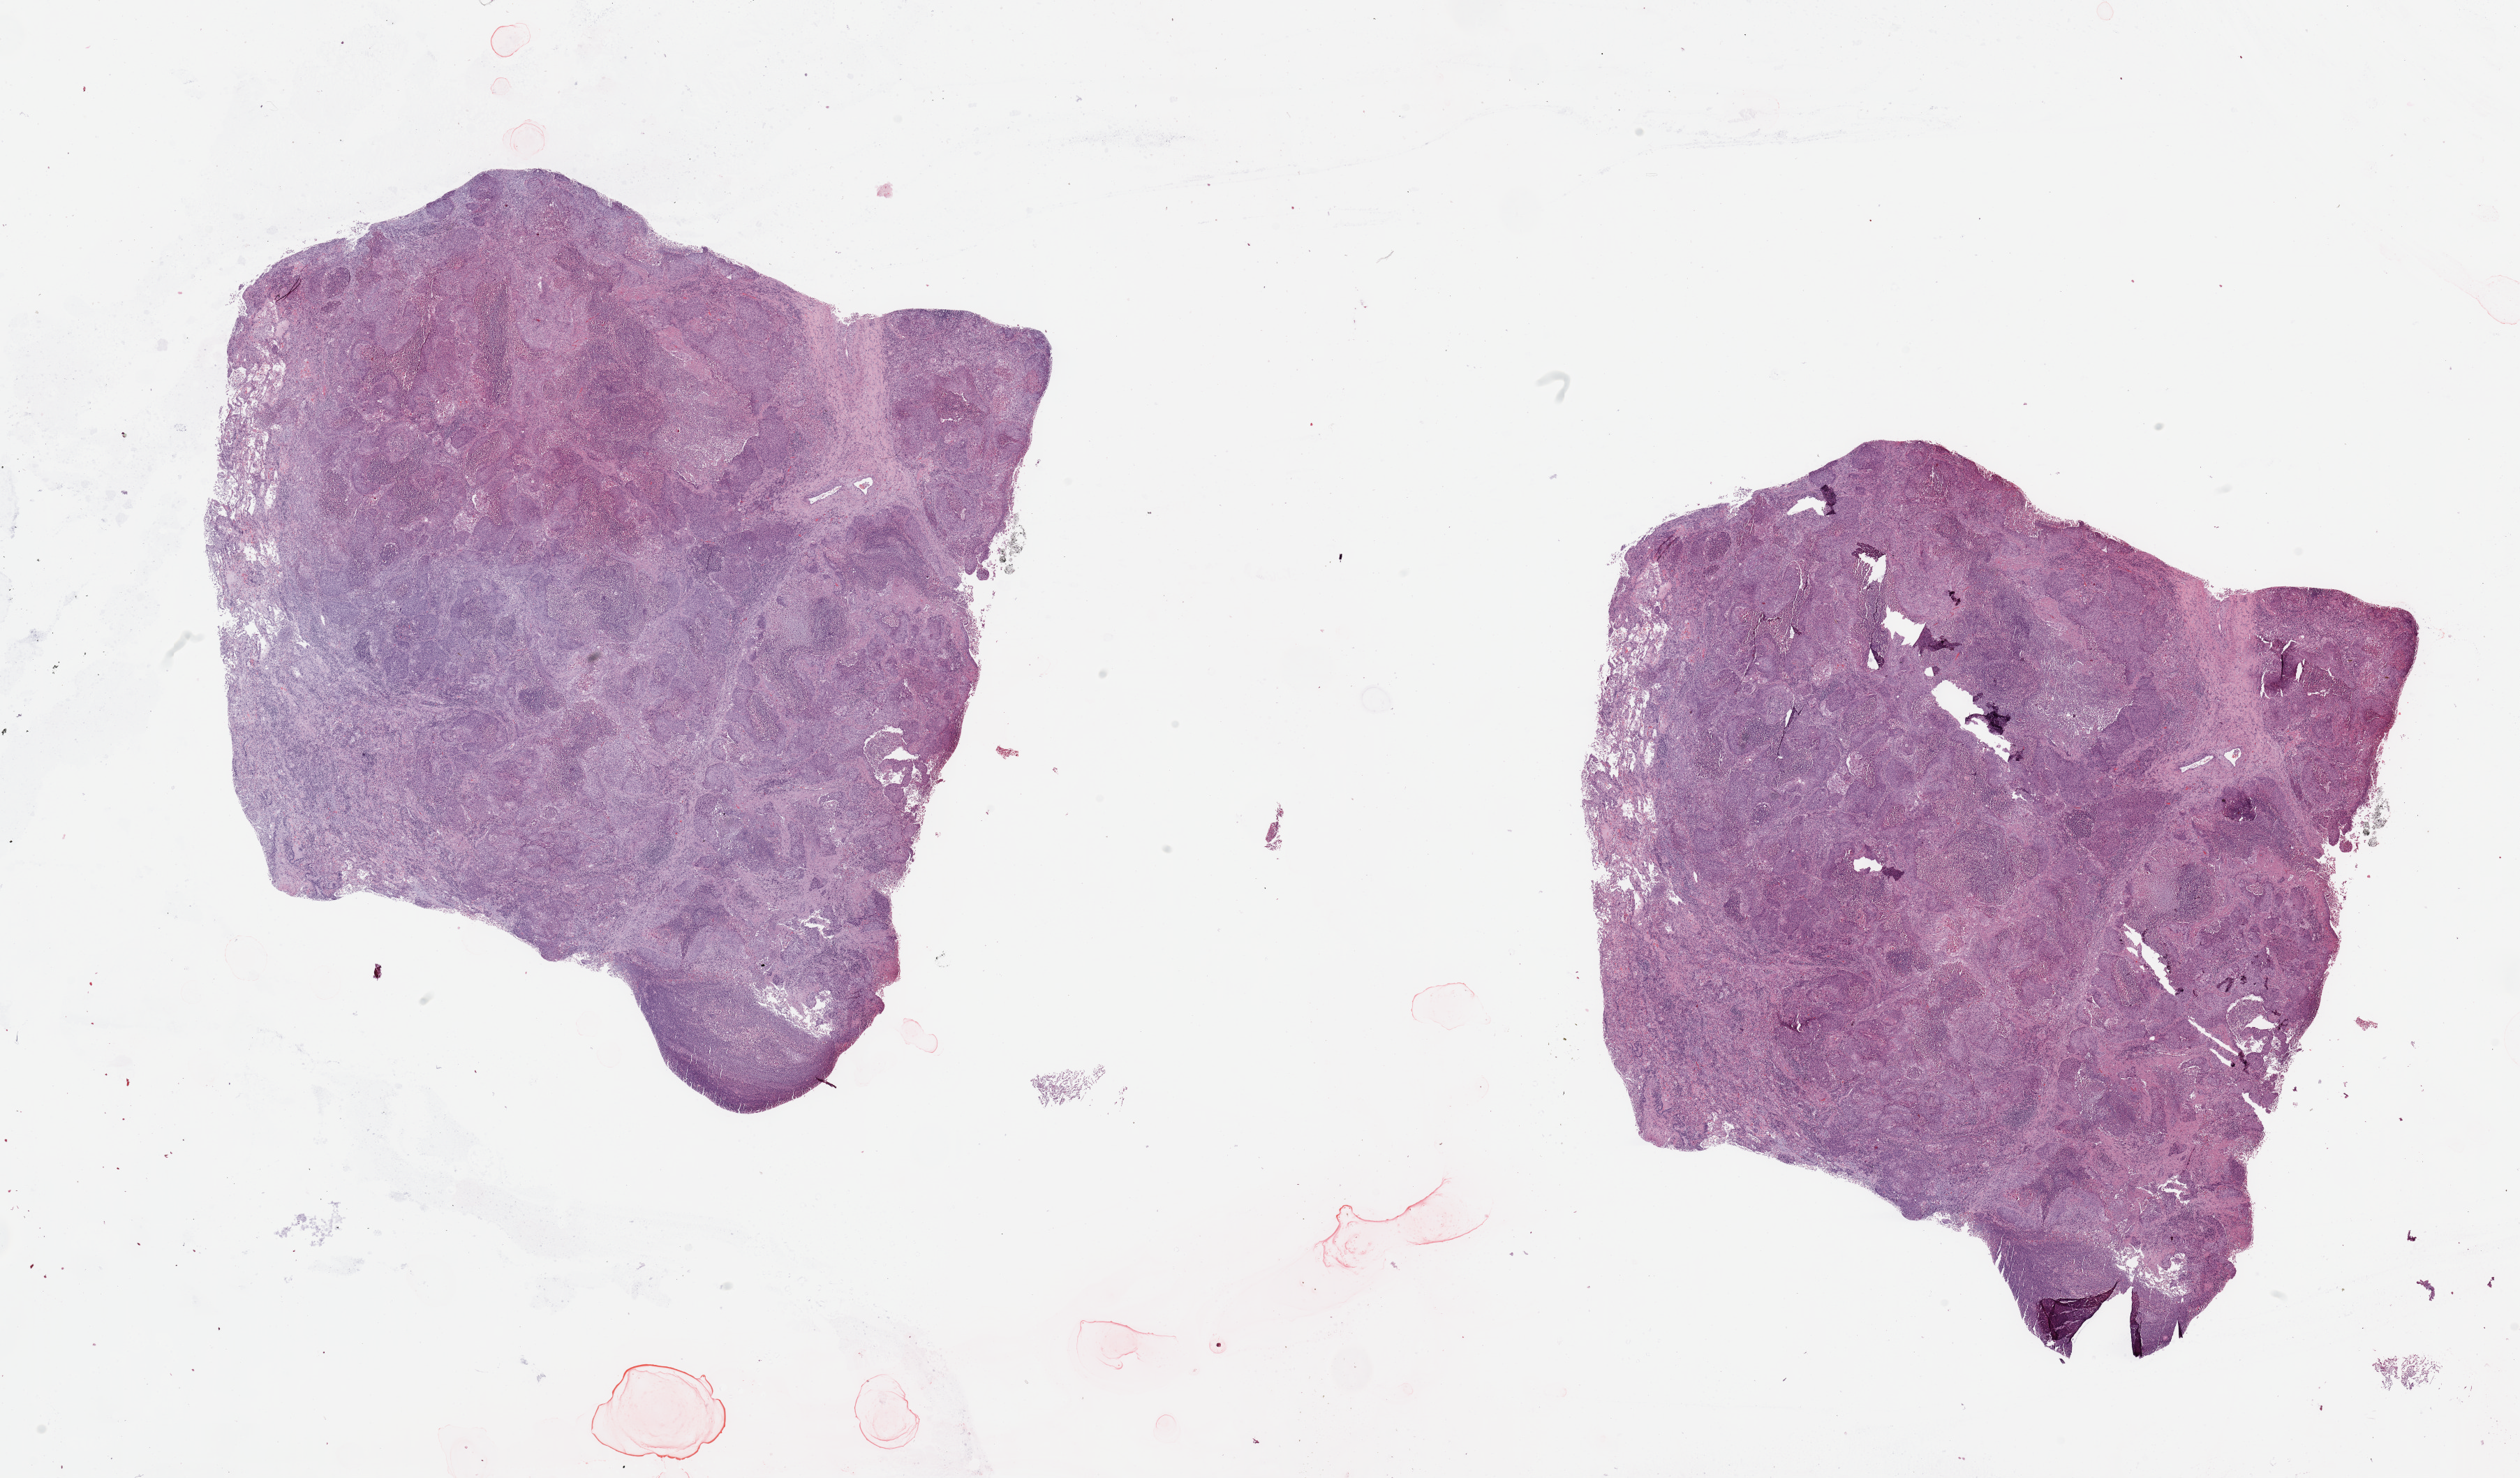
H&E whole-slide image — a low-resolution overview of the entire scanned area, about 28.5 x 16.7 mm; tumour tissue sample, sampled site: lung. Patient: male, age 70 years. Pathologist review of this section (percent, as recorded): tumour nuclei 60%, necrosis 15%.
Histologic diagnosis: Squamous cell carcinoma, NOS.